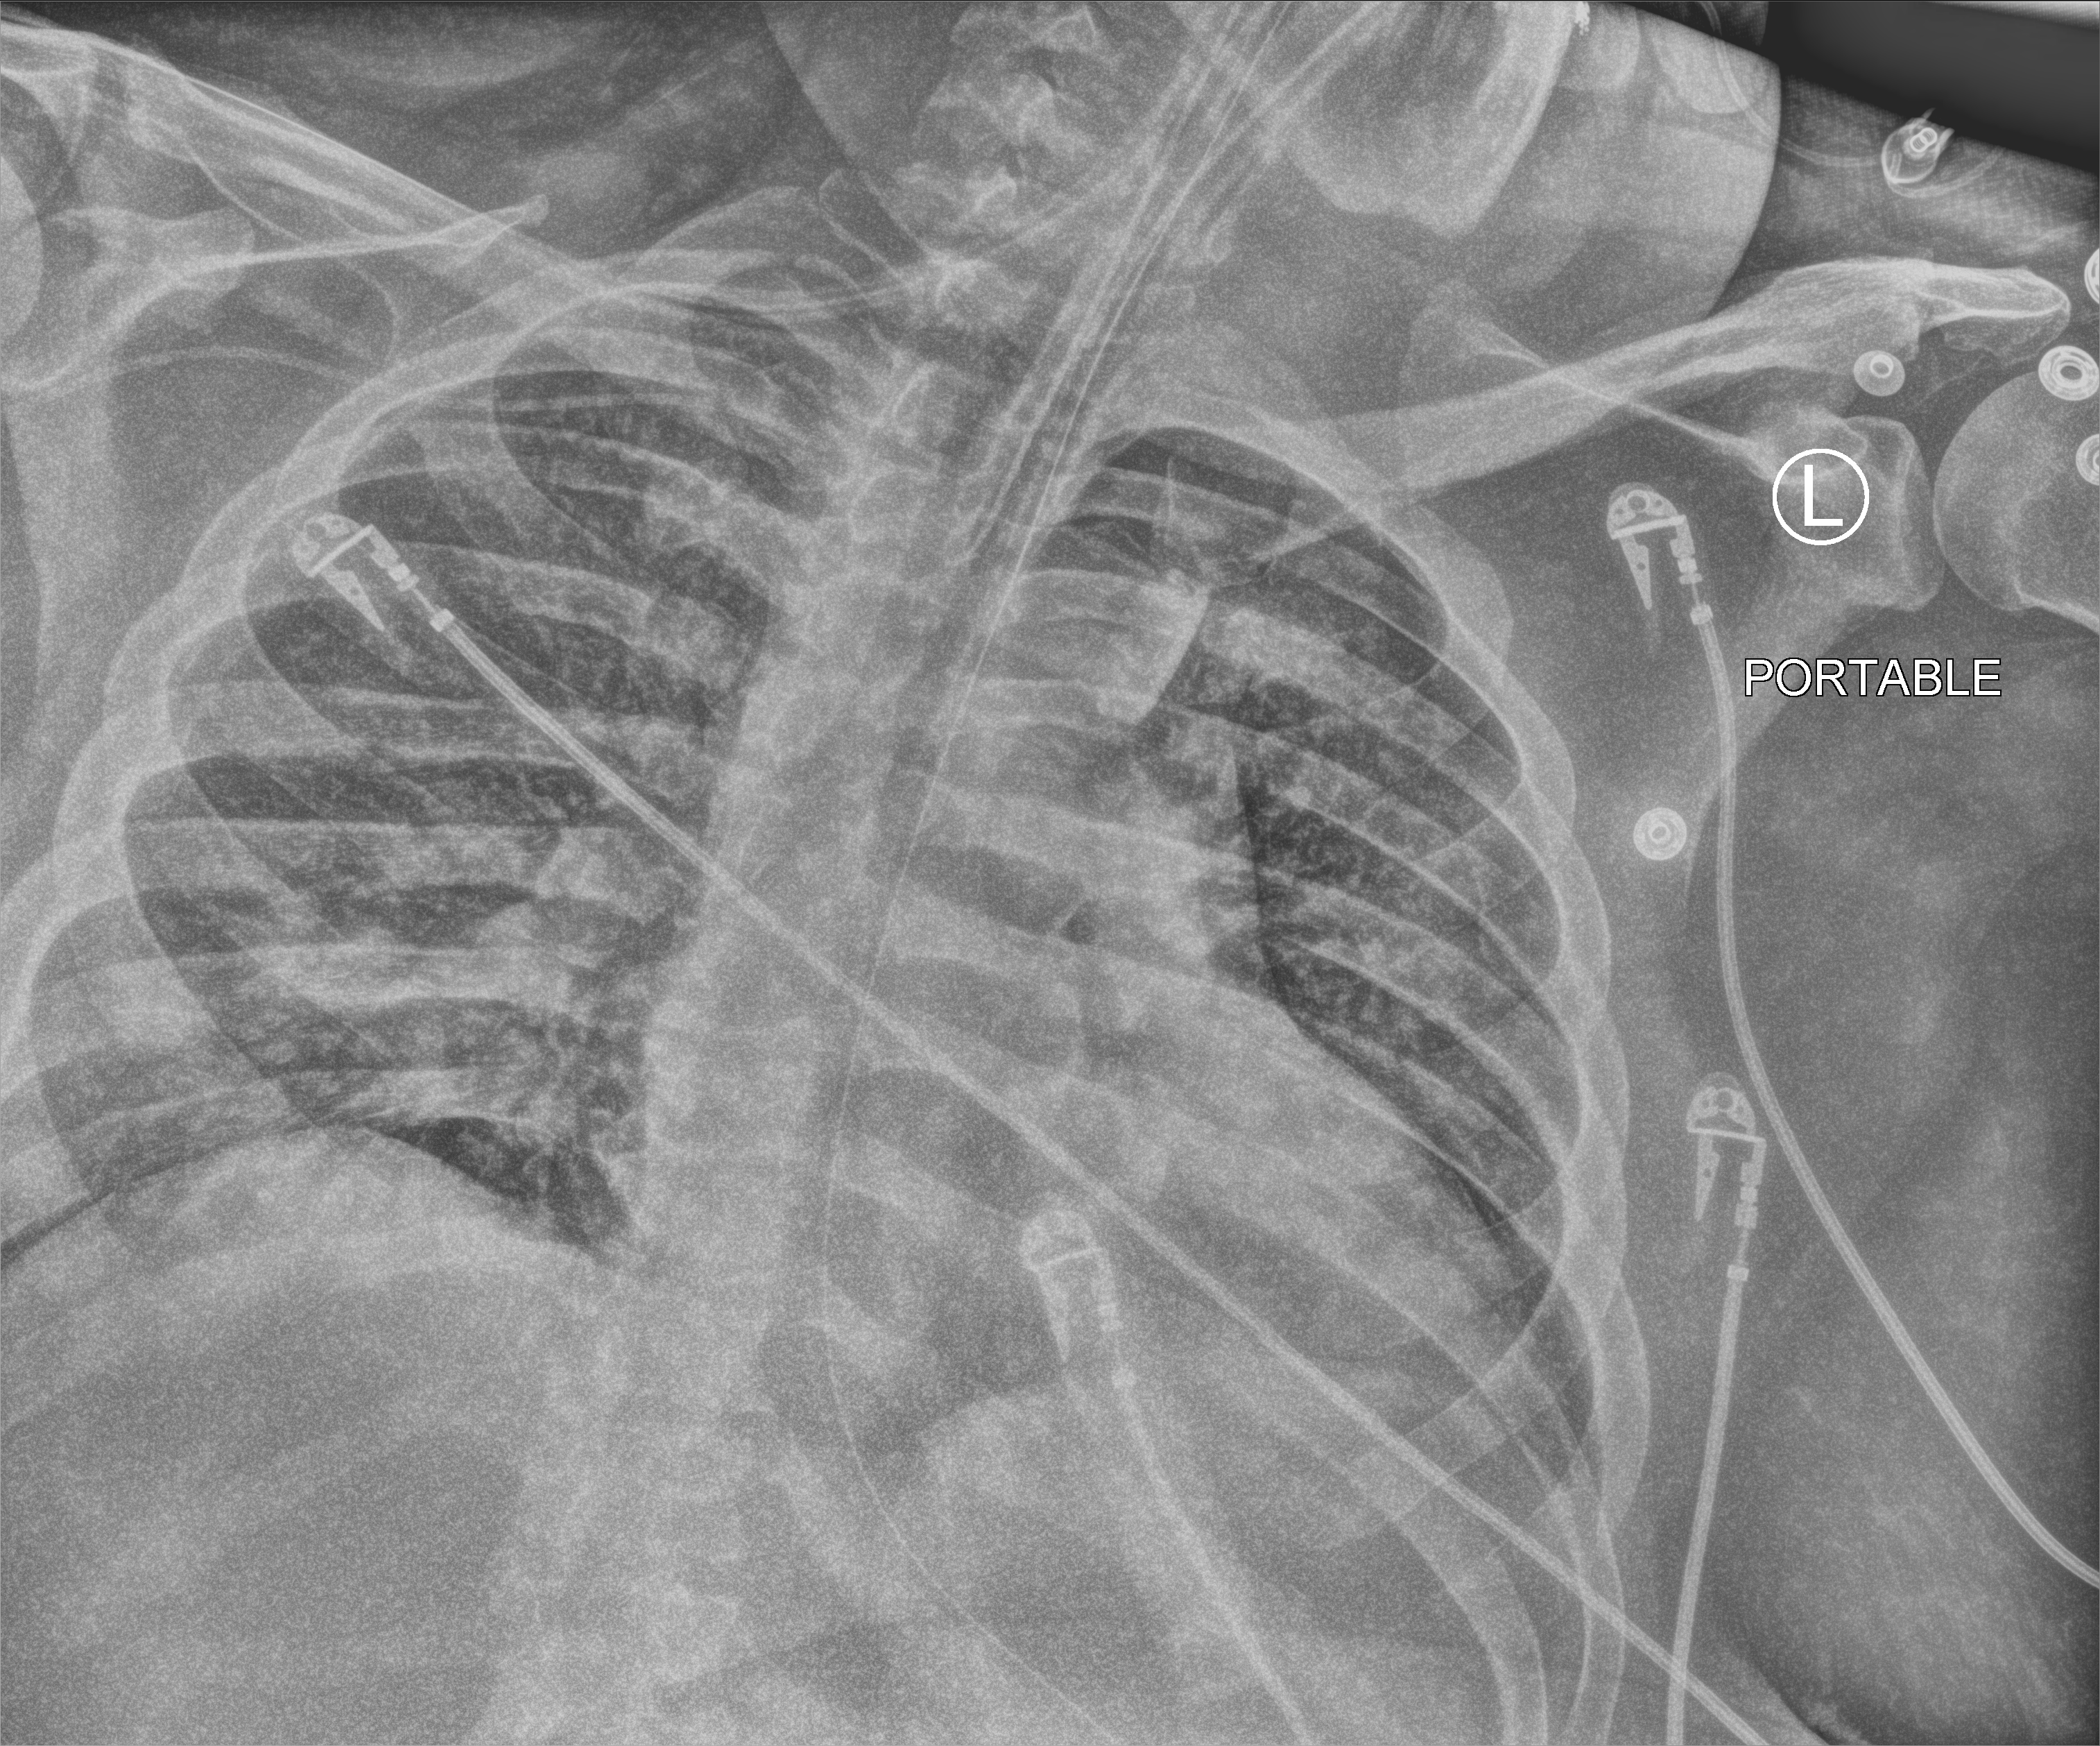
Chest X-ray (portable), anteroposterior (AP) projection. Adult patient hospitalised with COVID-19, age 18–59 years.
Admission-level facts for this patient (not findings on this image; timing relative to this image not recorded):
- admitted to intensive care during this hospital stay: yes
- diabetes (admission record): yes
- length of hospital stay: 10 days